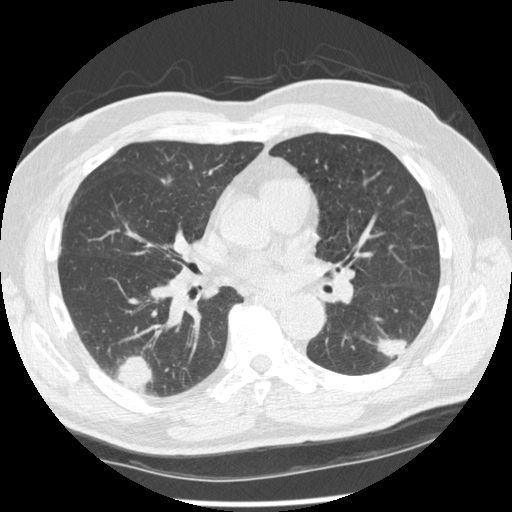
Low-dose screening chest CT, axial slice, second screening round (one year after baseline), lung window (W 1500 / L -600 HU), standard (soft-tissue) reconstruction kernel (STANDARD), 120 kVp, slice 120 of 227 in the series, 512 × 512 image matrix. Male, age 74 years at enrolment. Former smoker at enrolment.
- Expert reader's lesion annotation, box from (x=368, y=314) to (x=424, y=369) px.
- The screening reader recorded 7 non-calcified nodules or masses ≥4 mm on this exam; which of them this box marks is not recorded.
- Official screen result: positive, other.
- Later outcome: lung cancer diagnosed 43 days after this screen — squamous cell carcinoma, NOS, left lower lobe, well differentiated (G1), stage IA (AJCC 6th edition), 28 mm at pathology.